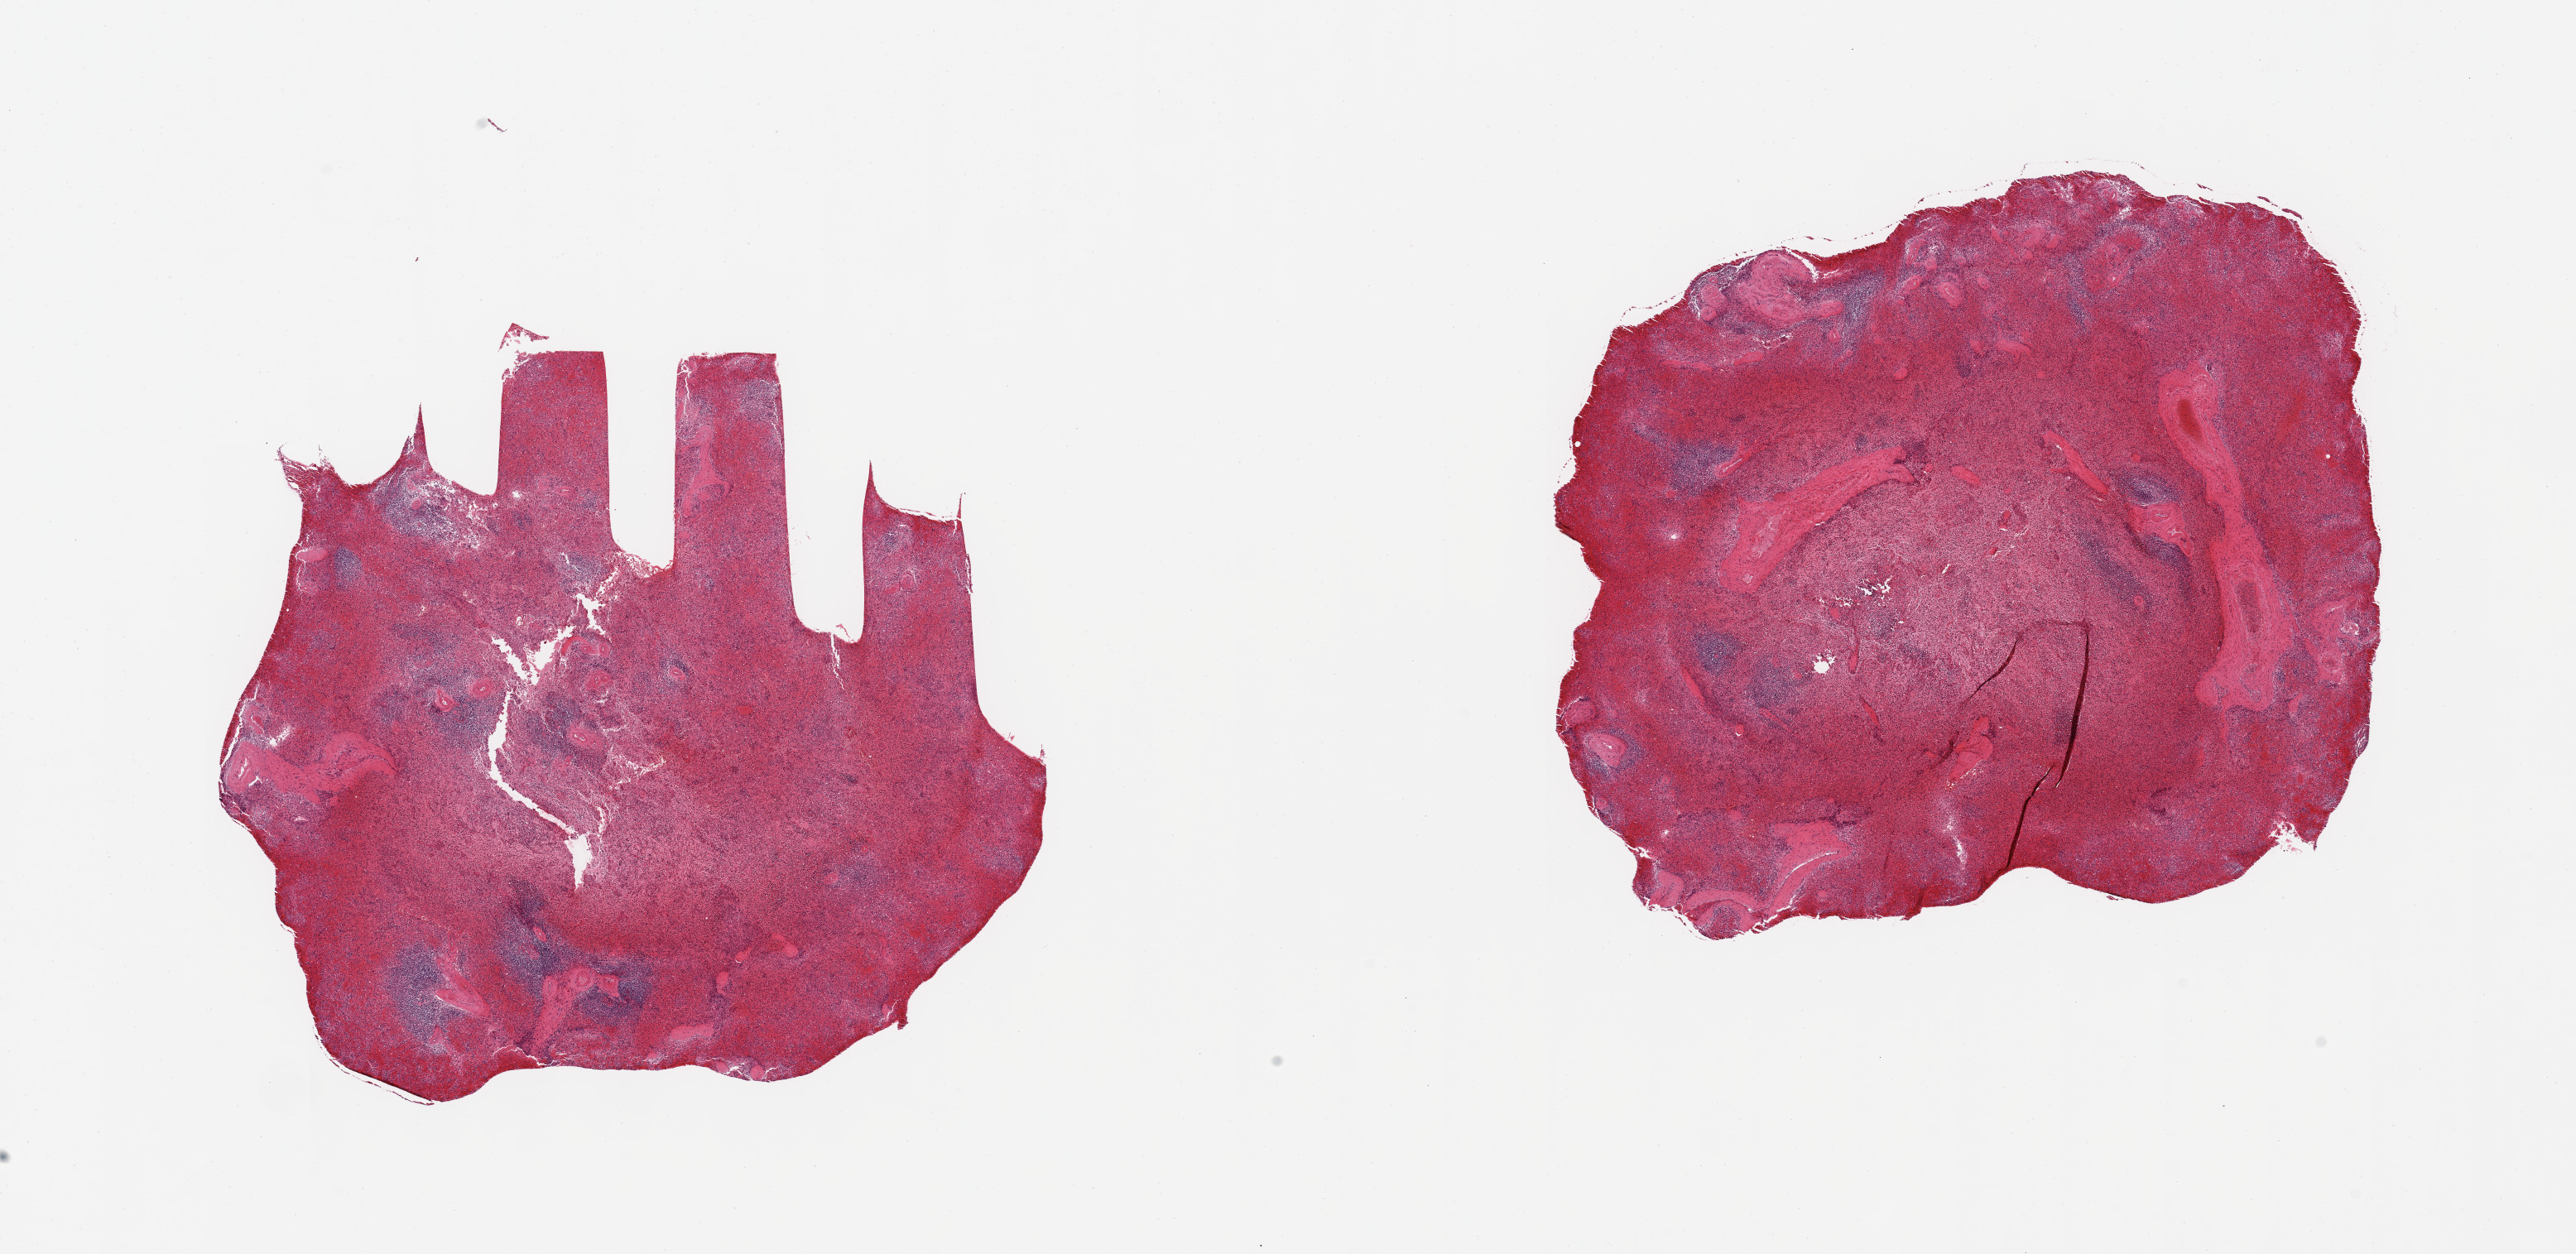
Whole-slide image, haematoxylin and eosin stain, brightfield — a low-resolution overview of the entire scanned area, about 24.6 x 12.0 mm, PAXgene-fixed, paraffin-embedded tissue, sampled site (target tissue): spleen, donor tissue sample. Female donor.
* reviewer comment on this tissue sample: 2 pieces; severe congestion